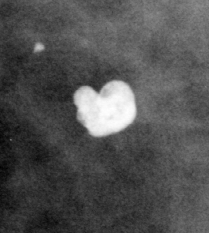
Crop from a digitized film mammogram around one marked abnormality; left breast; CC view; BI-RADS breast density category 3 (scale 1–4).
Marked abnormality: calcifications, morphology coarse; BI-RADS assessment category 2; benign without callback (not worked up further).